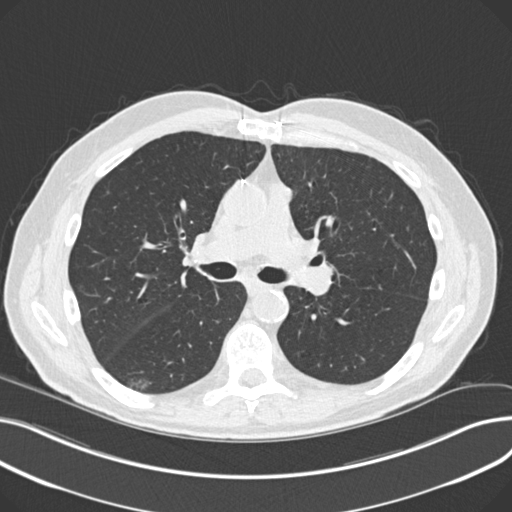
Low-dose screening chest CT, axial slice, third screening round (two years after baseline), lung window (W 1500 / L -600 HU), 2 mm slice thickness, standard (soft-tissue) reconstruction kernel (B30f), slice 101 of 230 in the series, 512 × 512 image matrix. Male, age 68 years at enrolment.
Expert-annotated lung lesion, bounding box [x1, y1, x2, y2] px = [121, 367, 167, 398]. The screening reader recorded 5 non-calcified nodules or masses ≥4 mm on this exam (right upper lobe, left upper lobe, right upper lobe, right lower lobe, right upper lobe); which of them this box marks is not recorded. Later outcome: lung cancer diagnosed 247 days after this screen — non-small cell carcinoma, right lower lobe, poorly differentiated (G3), stage IA (AJCC 6th edition), 23 mm at pathology.